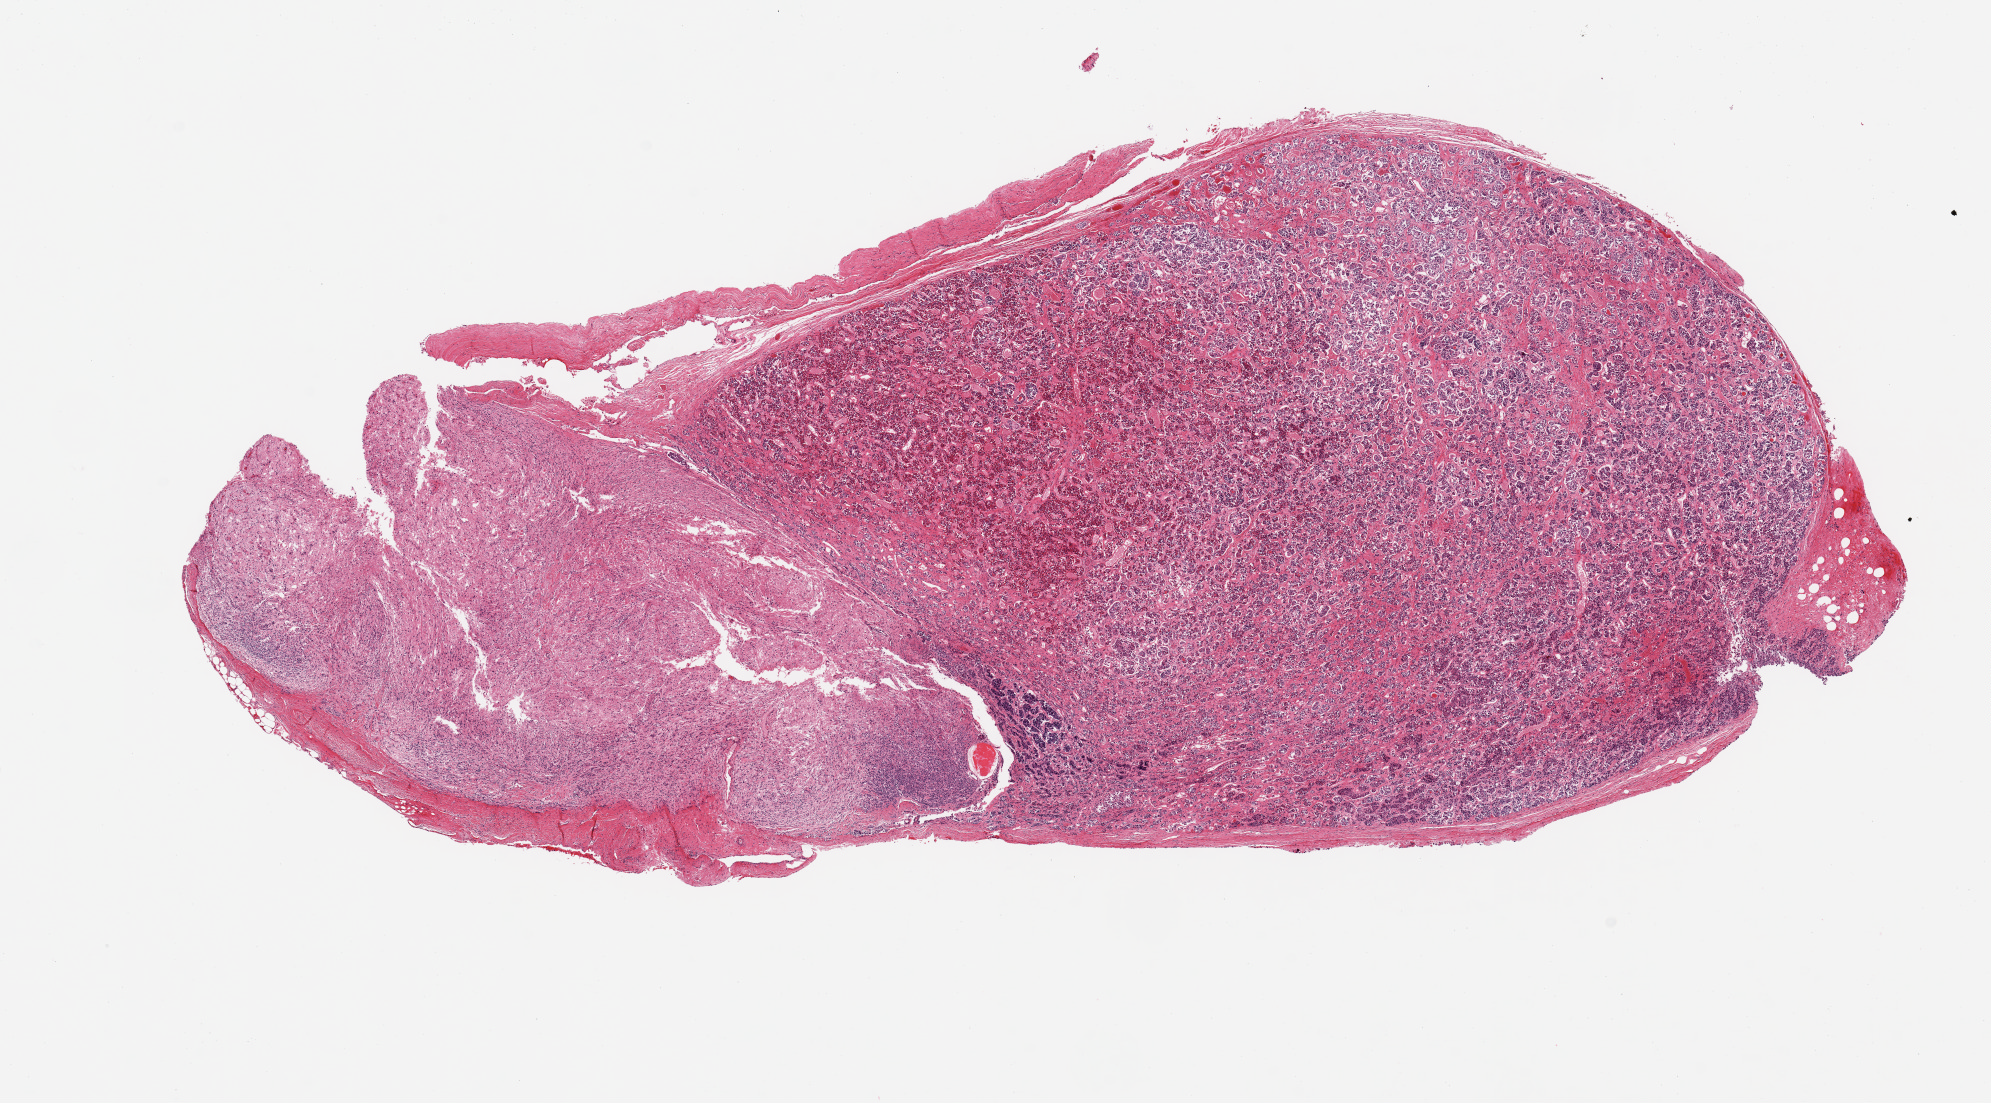
Hematoxylin and eosin (H&E) whole-slide image, brightfield, shown as a low-resolution overview of the whole scanned area (about 15.8 x 8.7 mm), PAXgene-fixed, paraffin-embedded tissue, sampled site (target tissue): pituitary, donor tissue sample.
Reviewer comment on this tissue sample: 1 piece, 25% neurohypophysis, remainder adenohypophysis.